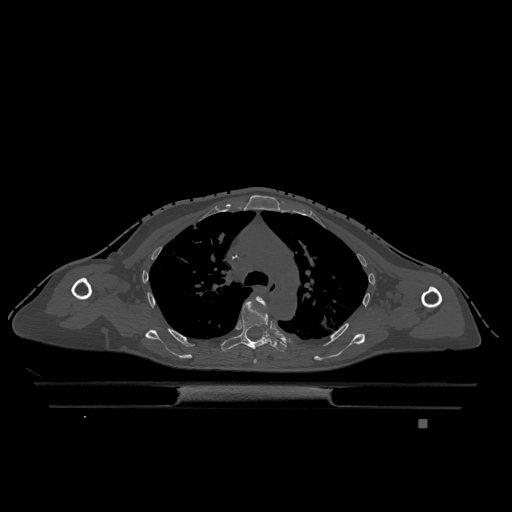
CT including the spine, one axial slice. Position 847 of 1317 along the scan axis. Bone window (W 1800 / L 400 HU). 0.5 mm slice thickness. 512 × 512 image matrix. Female patient, age 74 years. From the clinical record (not read from this slice): primary cancer: lung; vertebrae with lytic lesions (as recorded): T1, T4, T5, T6, L4, L5.
Outlined on this slice (semi-automatically segmented with operator editing):
- T4 vertebra: bounding box <253,297,267,363> (left, top, right, bottom; pixels)
- T5 vertebra: <221,301,287,353>